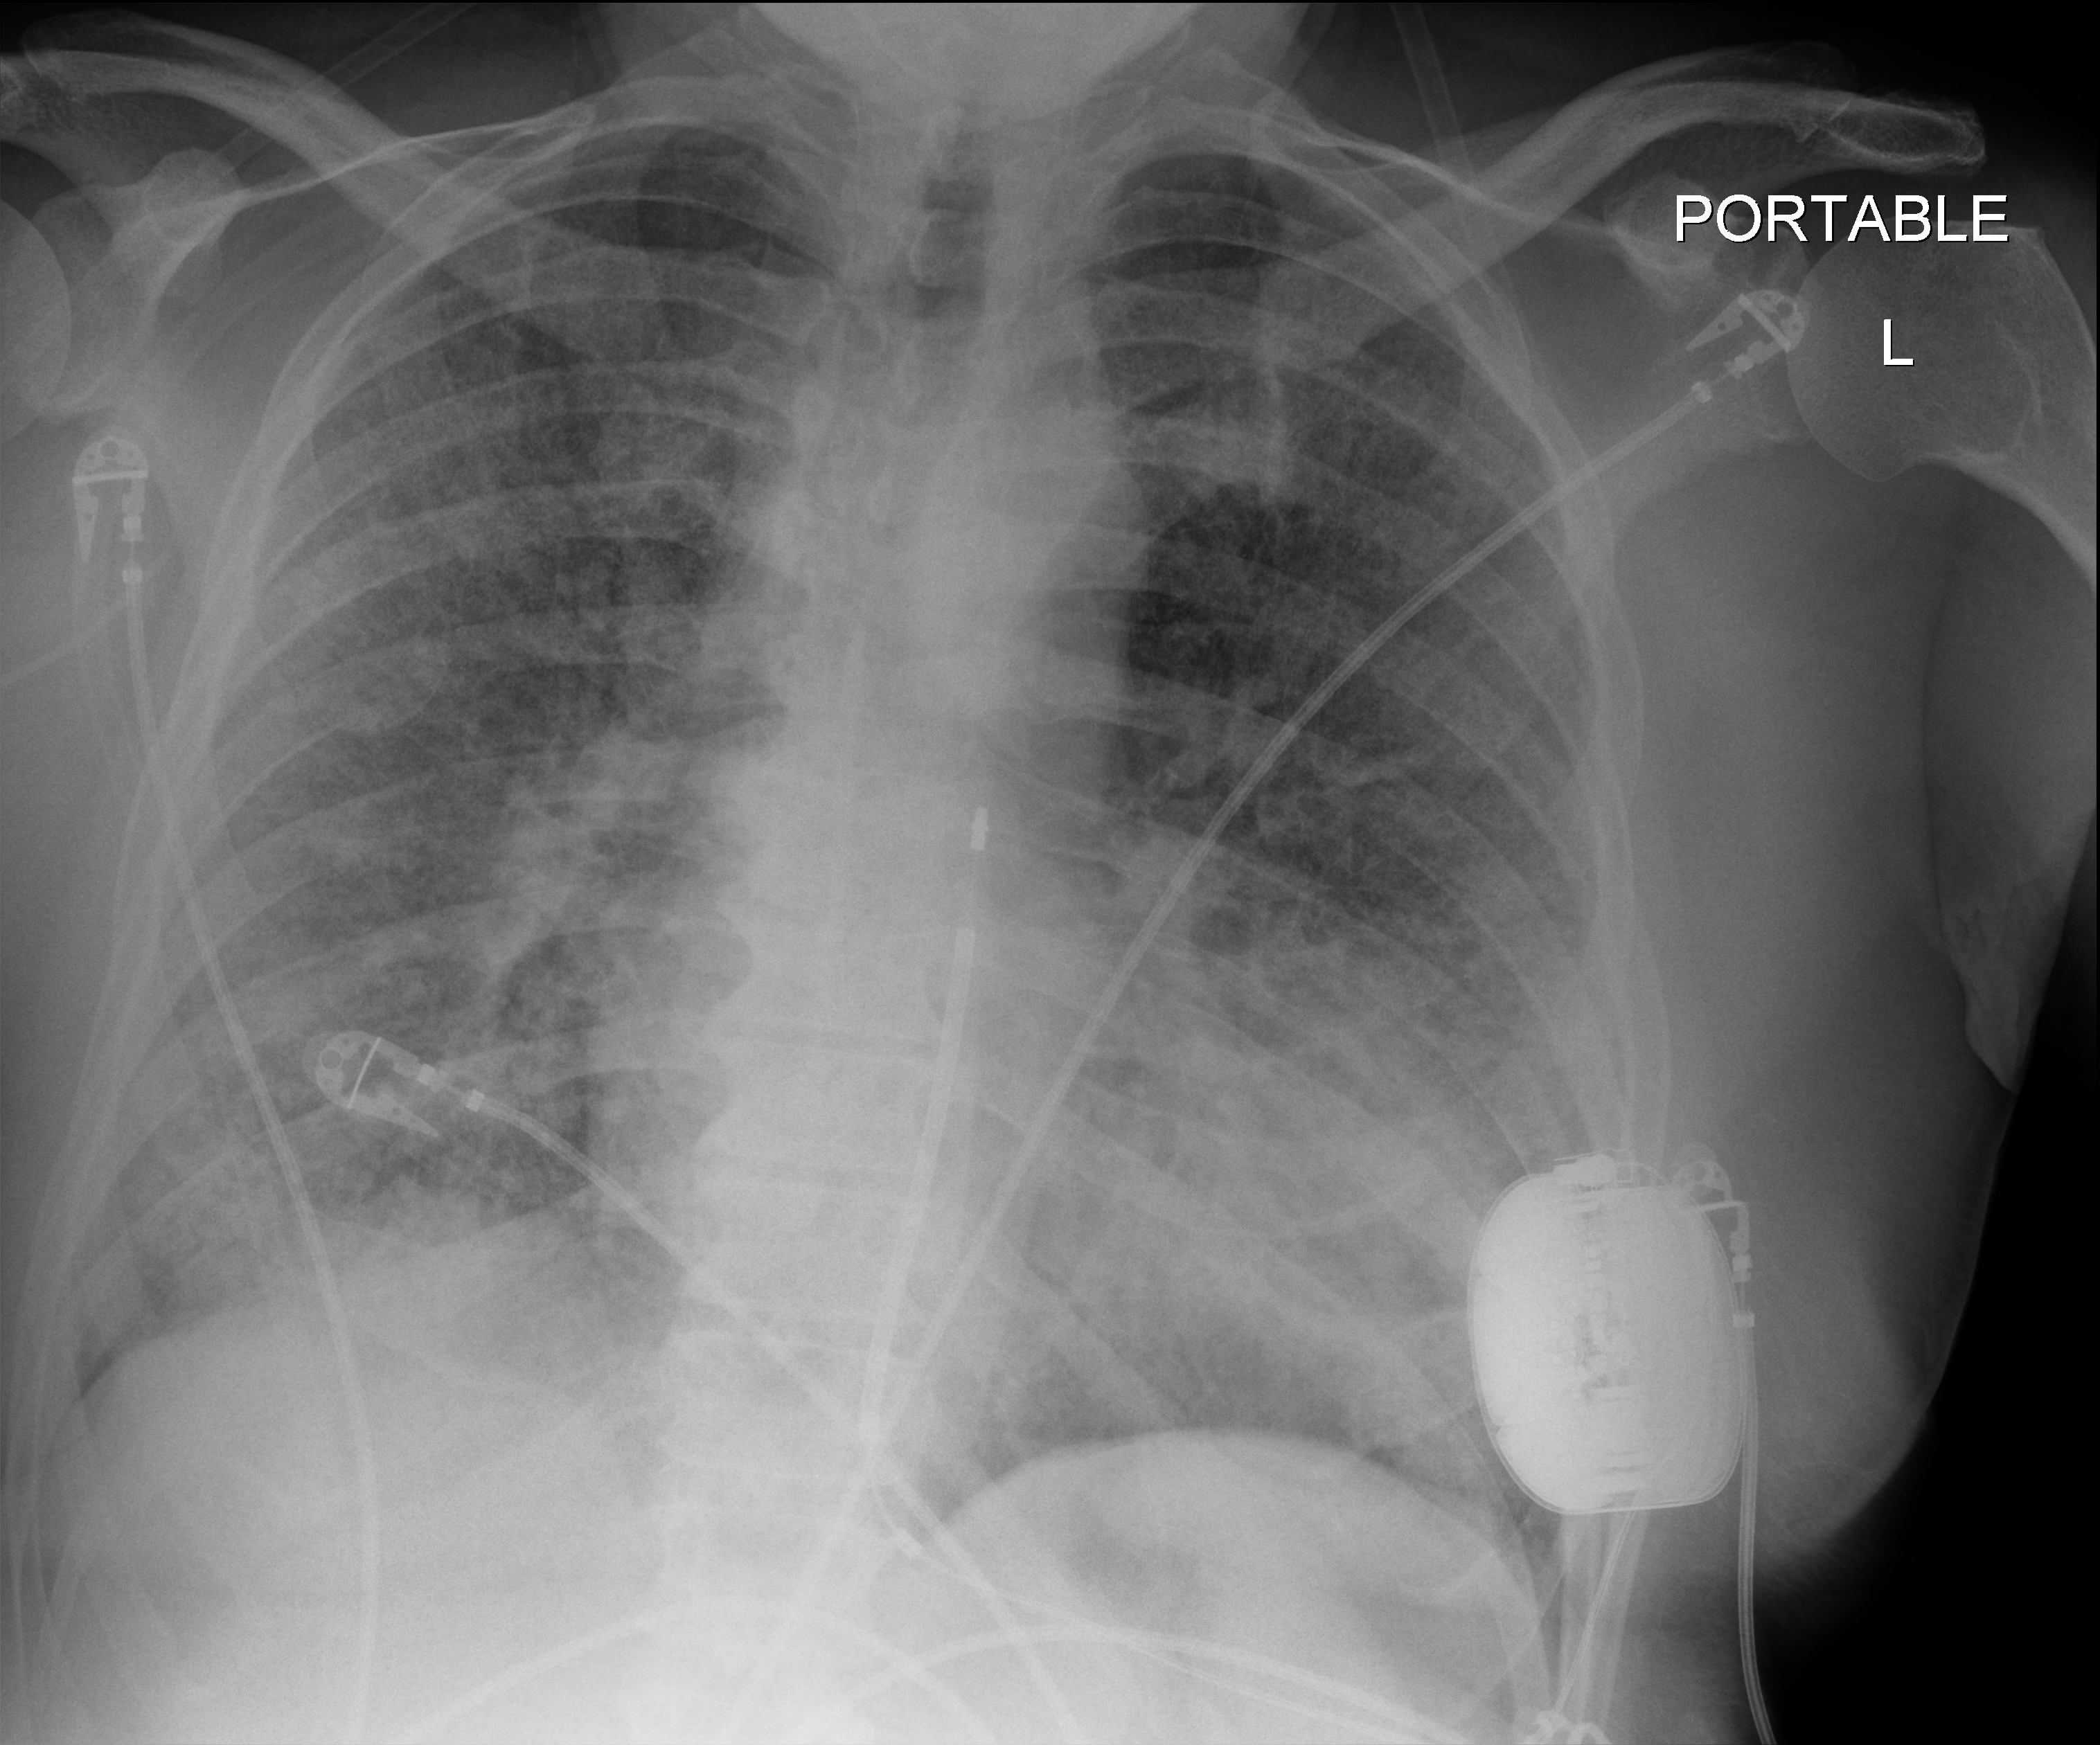
Chest X-ray (portable), anteroposterior (AP) projection. Patient hospitalised with COVID-19; male, aged 60–74 years.
From the hospital-stay record, not from the radiograph (when in the stay this image was taken is not recorded):
- mechanically ventilated during this hospital stay: yes
- length of hospital stay: 16 days
- admitted to intensive care during this hospital stay: yes